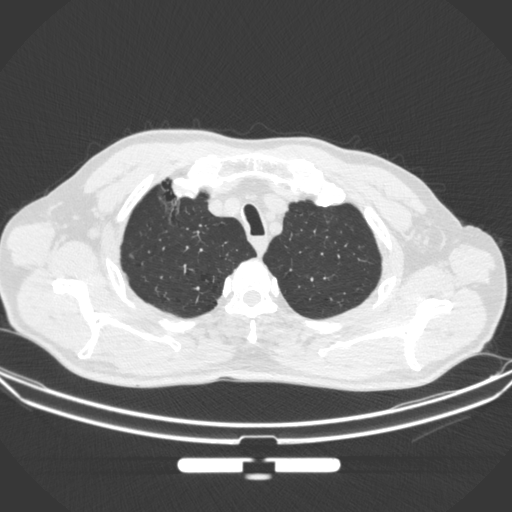
Chest CT, one axial slice; position 297 of 355 along the scan axis; 120 kVp; lung window (W 1500 / L -600 HU); 1 mm slice thickness; 512 × 512 image matrix, field of view 399 × 399 mm. Patient: male, 67 years. From the clinical record (not read from this slice): clinical TNM (as recorded): T1c N0 M0.
Annotated regions visible in this slice (bounding box drawn by a radiologist):
- lung tumour (recorded histology: adenocarcinoma): bounding box (x1, y1, x2, y2) in pixels: (150, 180, 197, 236)